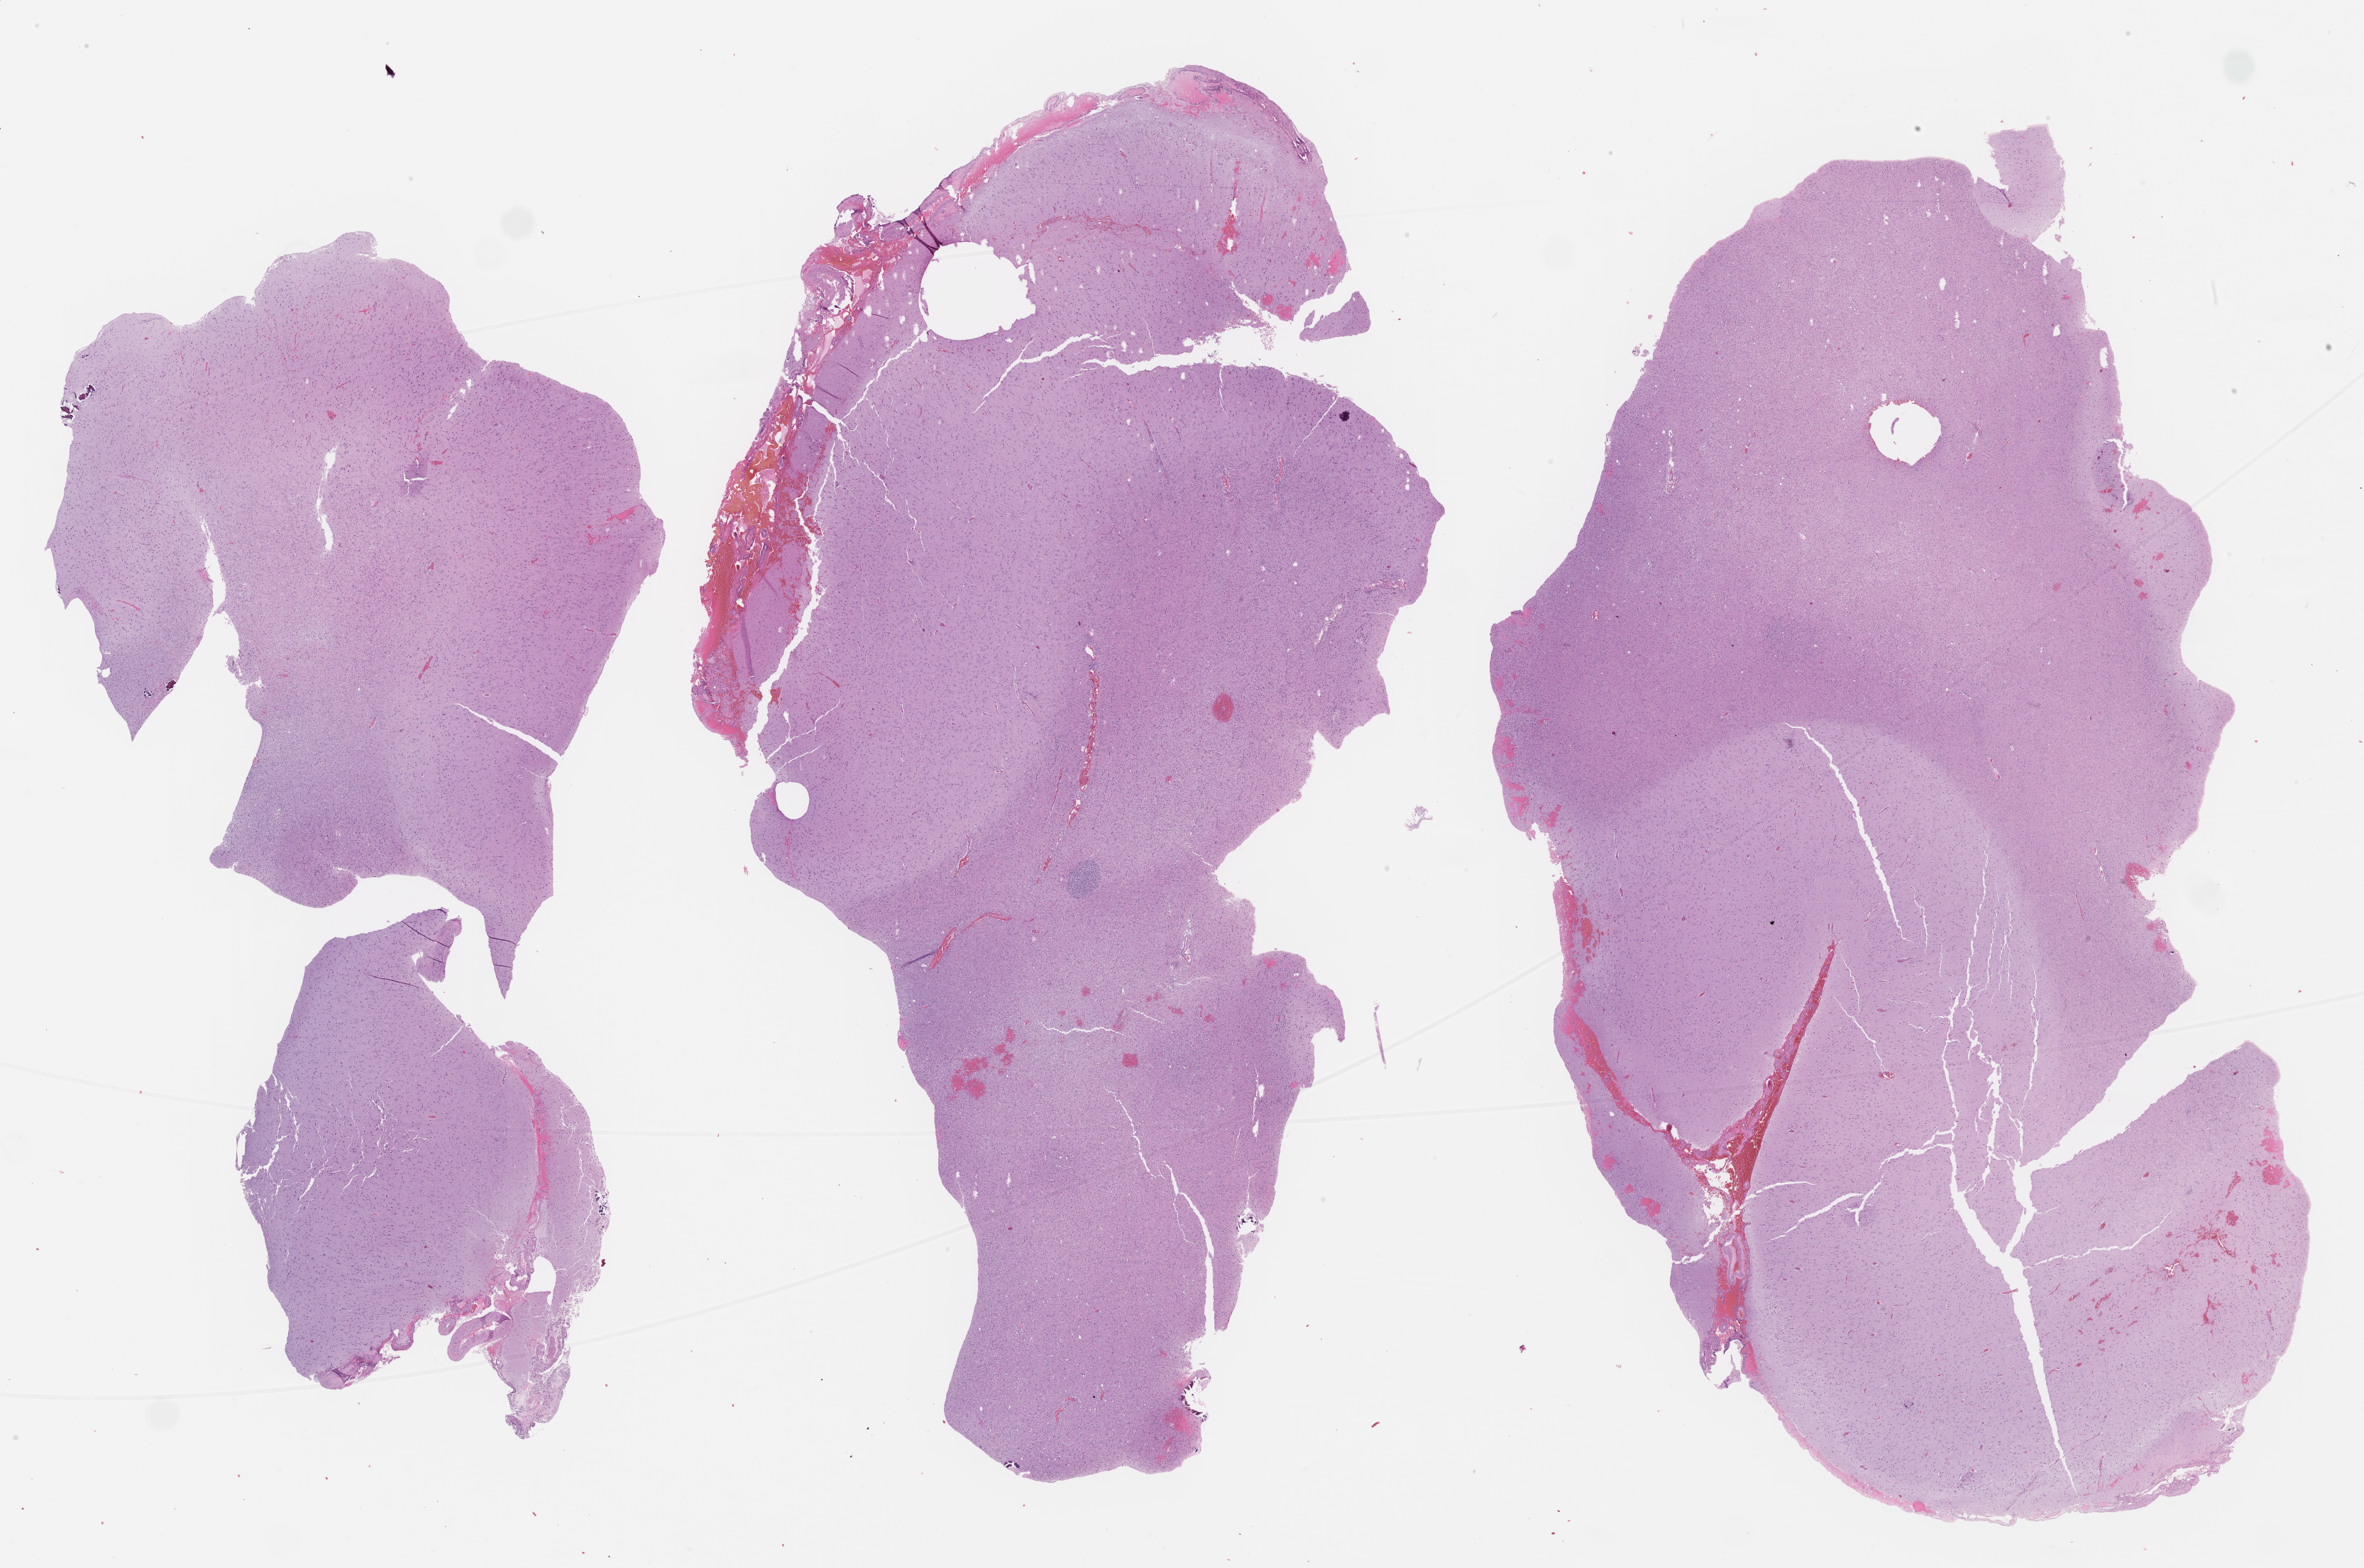
Whole-slide histology image, H&E — a low-resolution overview of the entire scanned area, about 26.8 x 17.8 mm (acquisition: 40x scan). Formalin-fixed paraffin-embedded (FFPE) diagnostic section. Brain, primary tumour sample. Patient: female, age at initial diagnosis 53 years. Histologic grade: G2 (moderately differentiated).
Histologic diagnosis: Oligodendroglioma, NOS (cerebrum).